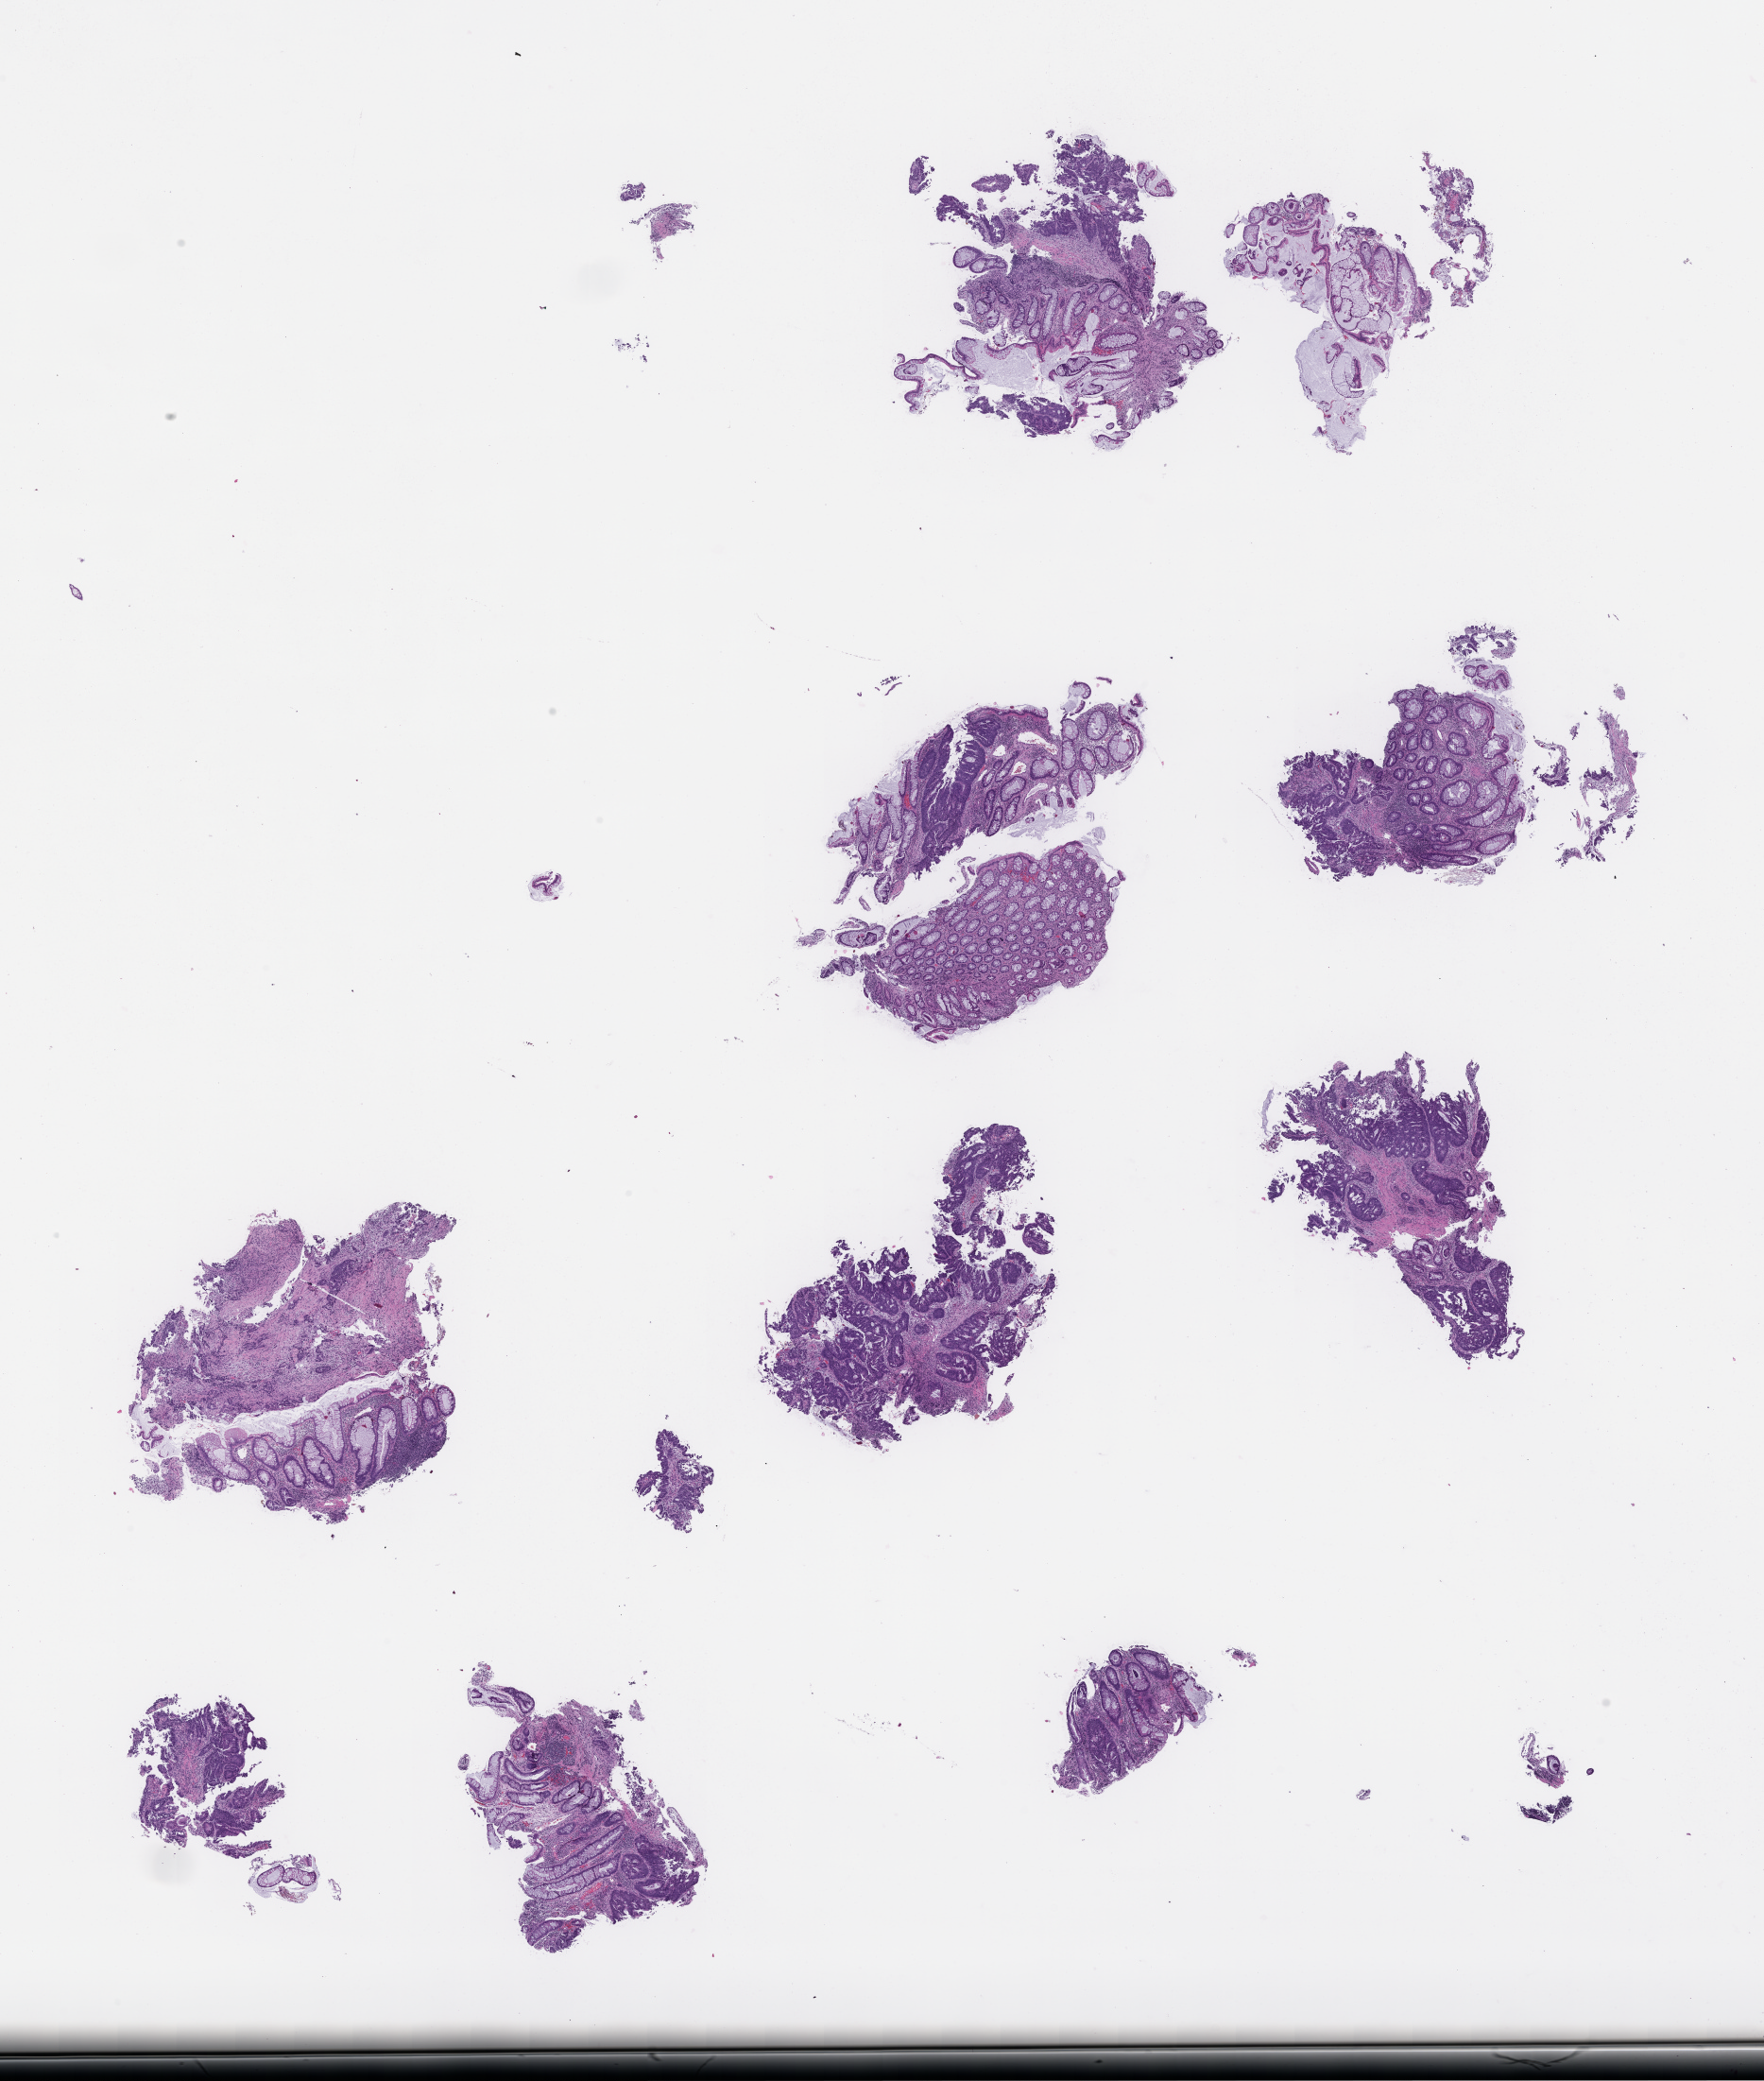
Whole-slide image, haematoxylin and eosin stain, a low-resolution overview of the entire scanned area, about 15.1 x 17.8 mm; formalin-fixed paraffin-embedded section; site: colon. Patient sex: male.
• this section: primary tumor
• diagnosis: Colorectal Carcinoma